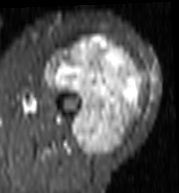
MRI of an extremity soft-tissue mass, one axial slice; position 57 of 103 along the scan axis; STIR; MR volume resampled by the dataset authors to the PET/CT grid (not the native acquisition matrix); 3.27 mm slice thickness; 179 × 193 image matrix, field of view 175 × 188 mm. Female patient. Case-level facts recorded for this patient, not image findings: histological type: undifferentiated – high grade; grade: high; site of the primary tumour: left thigh.
Structures marked on this image (expert contour drawn on MRI and transferred to this co-registered scan by the dataset authors):
- gross tumour volume including surrounding oedema: bounding box [x1, y1, x2, y2] px = [45, 37, 142, 156]
- gross tumour volume (mass): [45, 37, 142, 156]